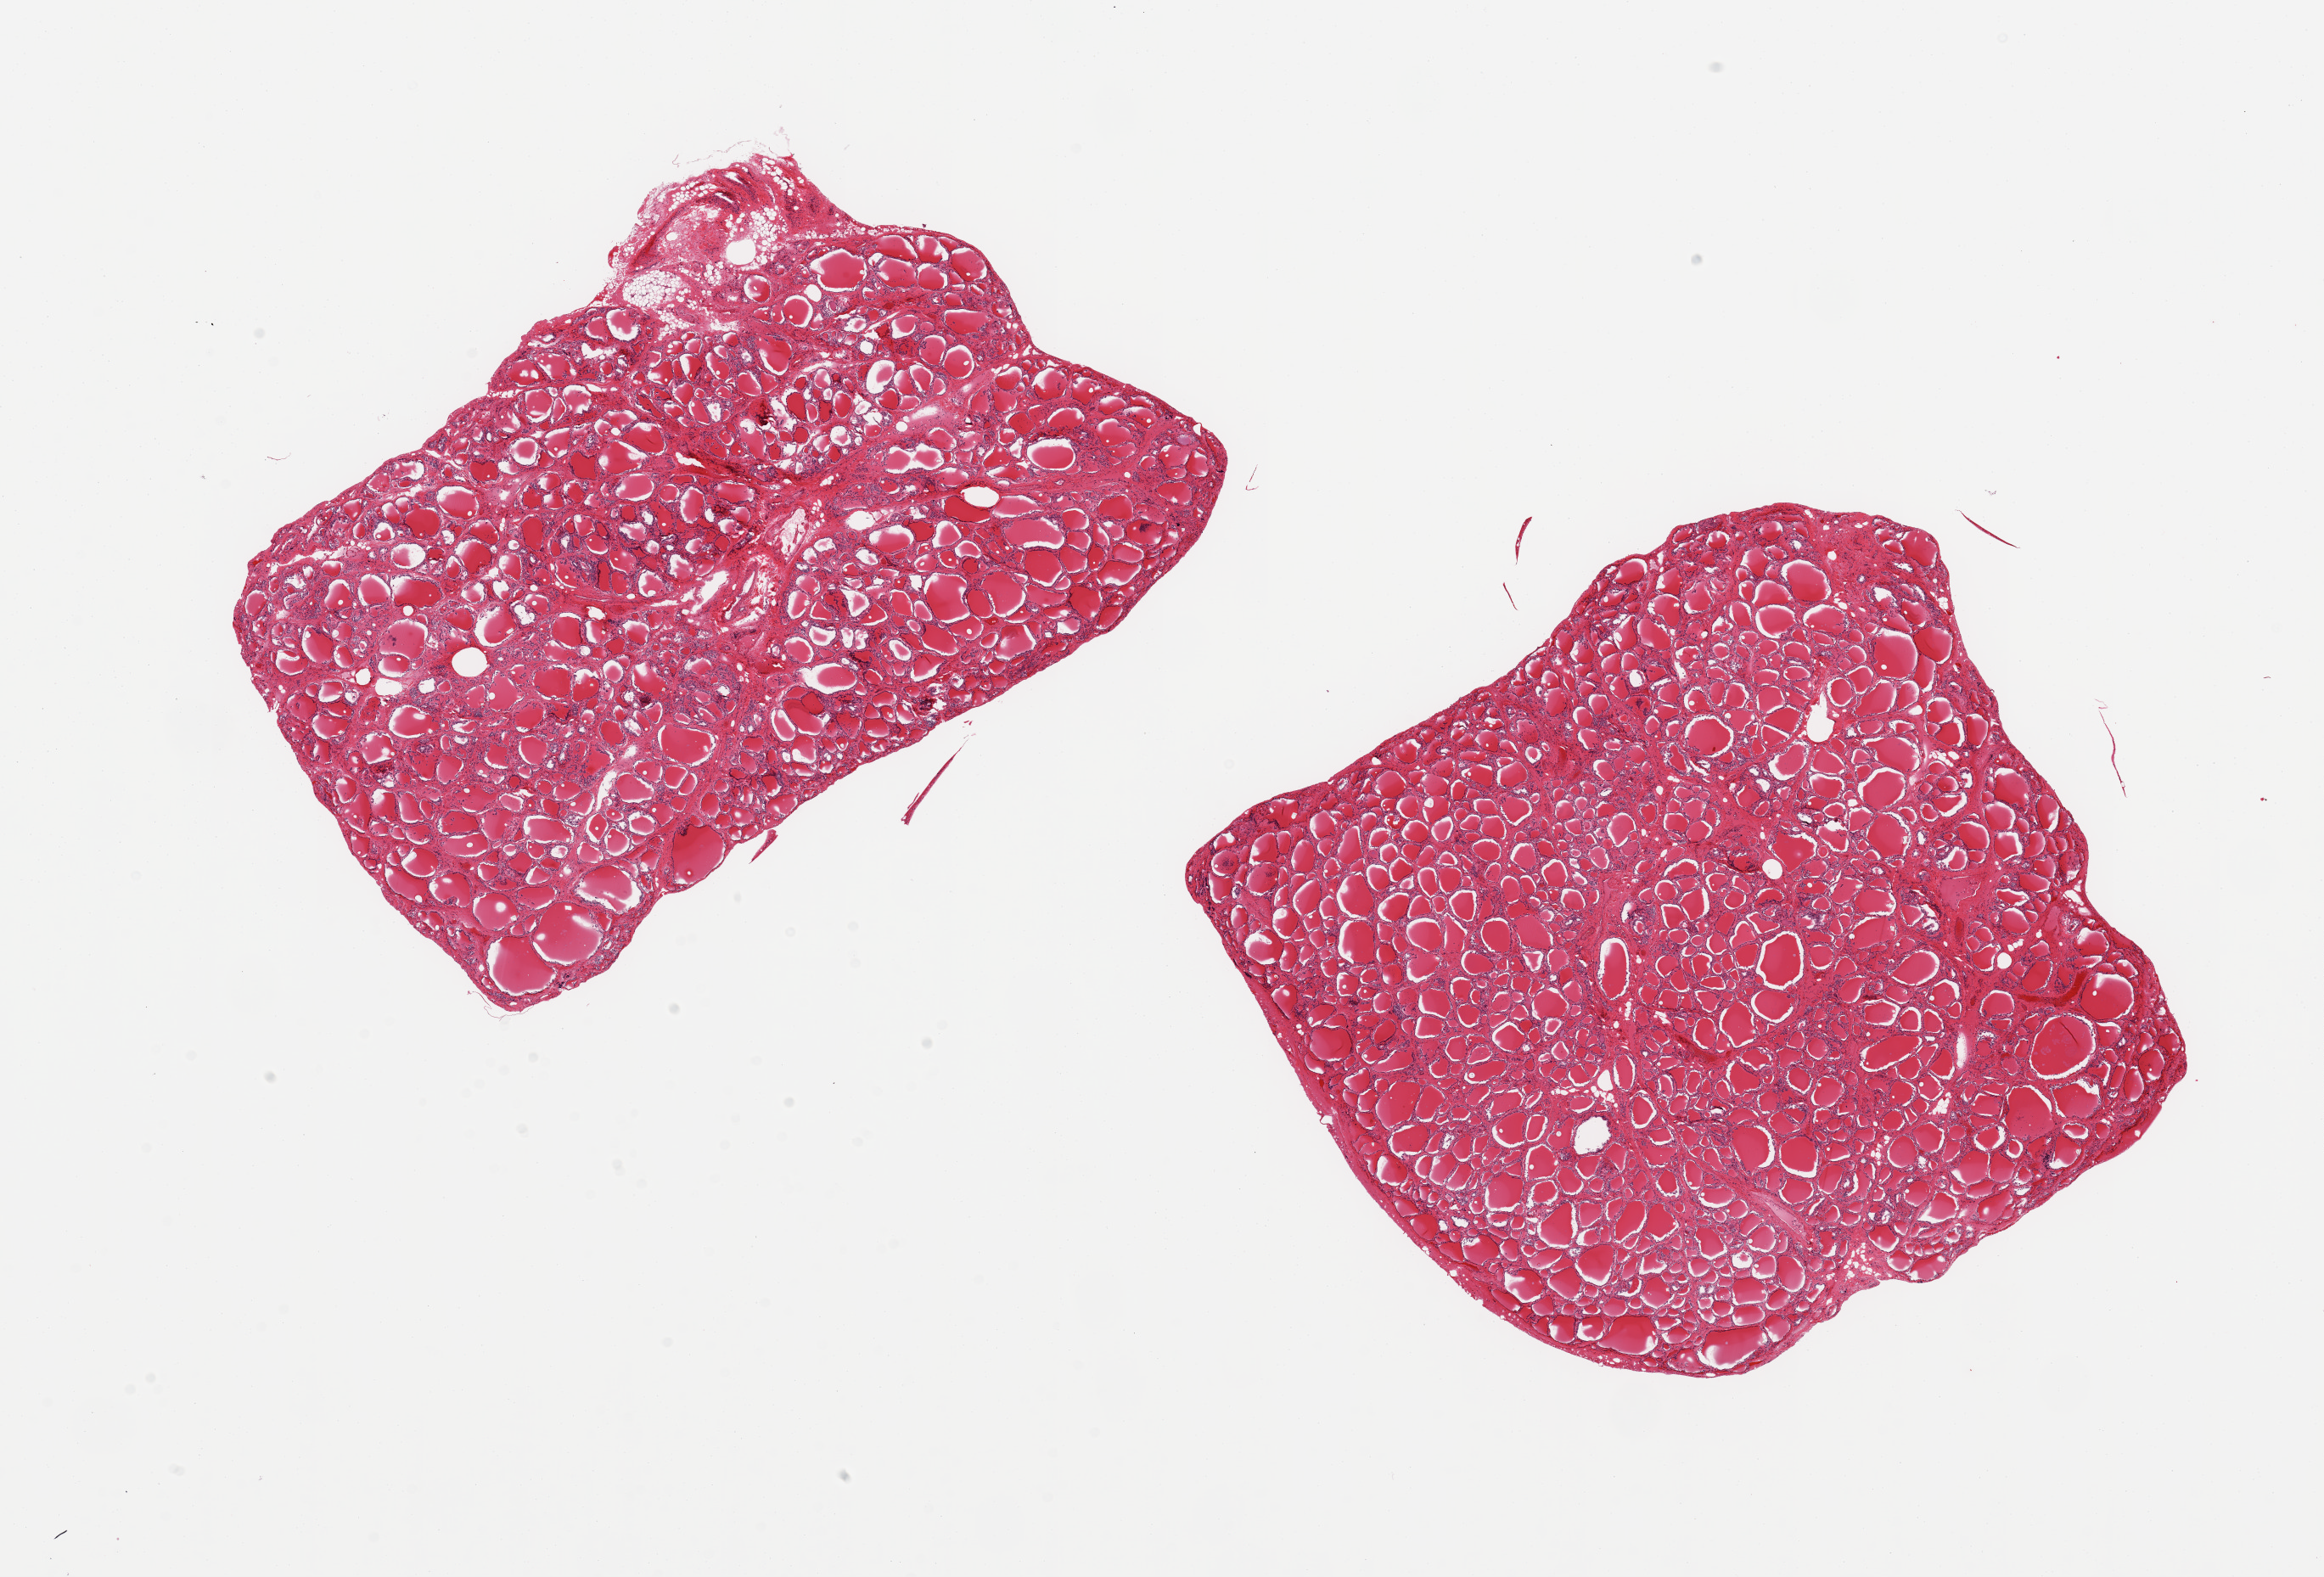
Haematoxylin and eosin whole-slide image, a low-resolution overview of the entire scanned area, about 21.7 x 14.7 mm; PAXgene-fixed paraffin-embedded (PFPE) section; target tissue: thyroid; tissue donor sample.
• reviewer comment on this tissue sample: 2 pieces, no abnormalities